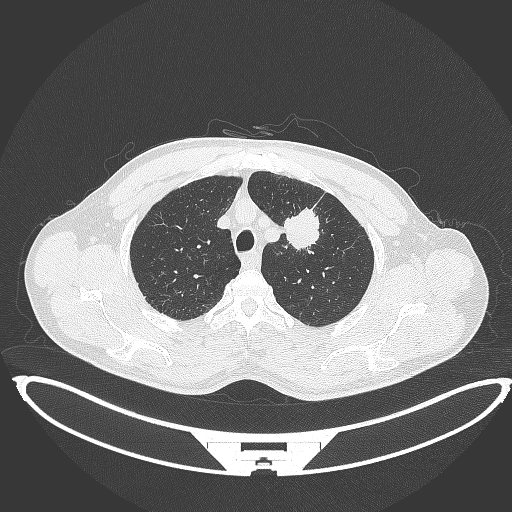
Chest CT, one axial slice; slice 356 of 395 in the series (ordered by position); reconstruction kernel B70f; 120 kVp; lung window (W 1500 / L -600 HU); 1 mm slice thickness; 512 × 512 image matrix, field of view 457 × 457 mm. Male patient, age 60 years. Case-level facts recorded for this patient, not image findings: clinical TNM (as recorded): T2a N0 M0; histopathological grade: G1-G2.
Outlined on this slice (rectangle marked by the reading radiologist):
- lung tumour (recorded histology: squamous cell carcinoma): bounding box (x1, y1, x2, y2) in pixels: (282, 204, 323, 252)